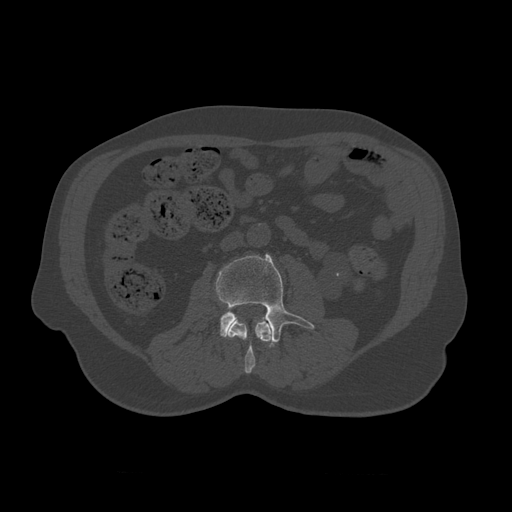
CT including the spine, one axial slice. Slice 313 of 450 in the series (ordered by position). 120 kVp. Bone window (W 1800 / L 400 HU). 512 × 512 image matrix. Patient age 75 years. From the clinical record (not read from this slice): primary cancer: prostate.
Outlined on this slice (semi-automatic segmentation, software-assisted and operator-edited):
- L2 vertebra: box from (x=226, y=316) to (x=272, y=374) px
- L3 vertebra: (x=215, y=253)–(x=315, y=348)